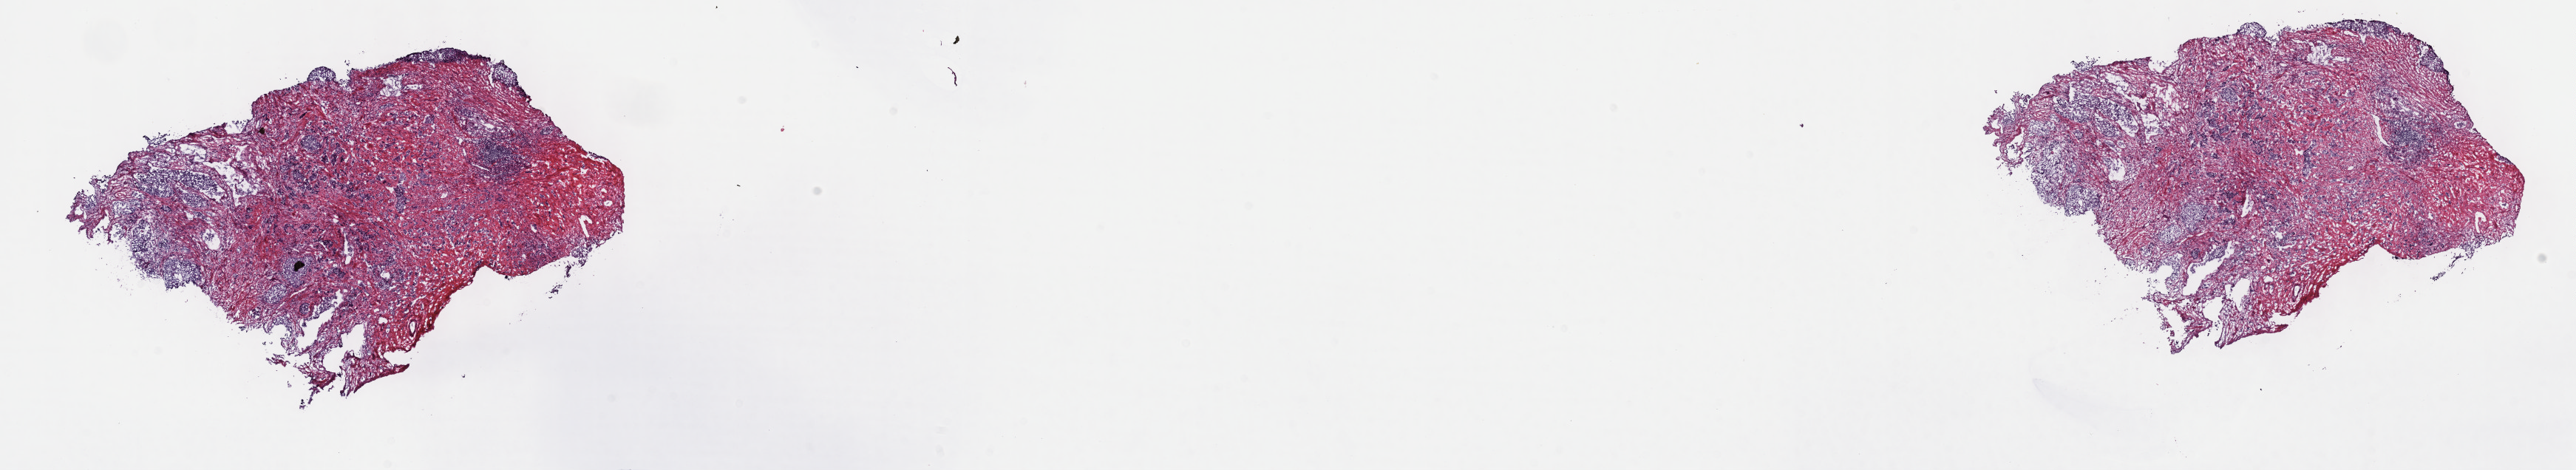
Digitized Hematoxylin and eosin (H&E) stained tissue section (whole slide) — low-resolution overview of the scanned area, about 28.2 x 5.1 mm (slide scanned at 40x). Frozen section. Primary tumour sample from the prostate. Patient: male, age at initial diagnosis 64 years. Gleason score: 9 (5+4). Composition of this section per pathologist review: tumour cells 60%, tumour nuclei 60%, normal cells 0%, stromal cells 40%, necrosis 0%. Infiltration values recorded for this section: lymphocyte infiltration 40%, monocyte infiltration 20%, neutrophil infiltration 20%.
Histologic diagnosis: Adenocarcinoma, NOS.